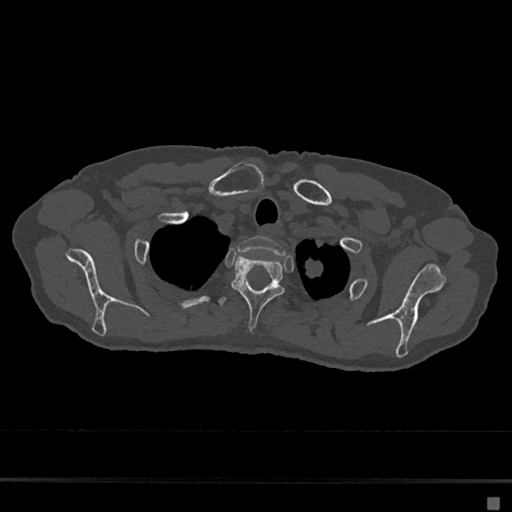
CT including the spine, one axial slice. Position 574 of 797 along the scan axis. Reconstruction kernel Br40s/3. Bone window (W 1800 / L 400 HU). 0.5 mm slice thickness. 512 × 512 image matrix, field of view 360 × 360 mm. Female patient, age 68 years. Case-level facts recorded for this patient, not image findings: primary cancer: renal.
Structures marked on this image (semi-automatic segmentation, software-assisted and operator-edited):
- T1 vertebra: bounding box (x1, y1, x2, y2) in pixels: (237, 236, 285, 255)
- T2 vertebra: (232, 255, 285, 331)
- T3 vertebra: (218, 297, 227, 307)